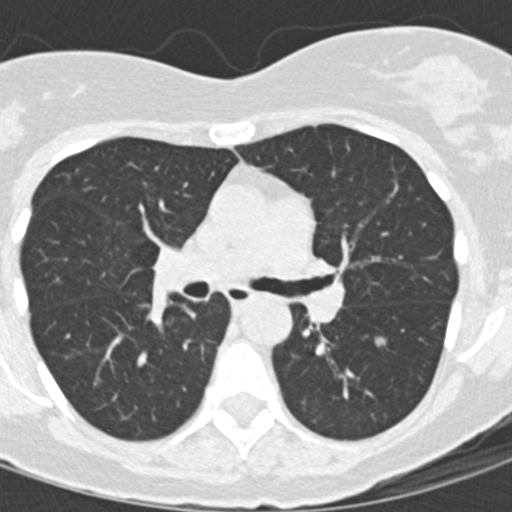
Low-dose screening chest CT, one axial slice. Slice 87 of 145 in the series (ordered by position). Reconstruction kernel B30f. Lung window (W 1500 / L -600 HU). 2 mm slice thickness. 512 × 512 image matrix, field of view 270 × 270 mm.
Outlined on this slice (outlined manually by an expert reader):
- lesion 1 (tumor, lower lobe of left lung): box from (x=375, y=337) to (x=386, y=346) px